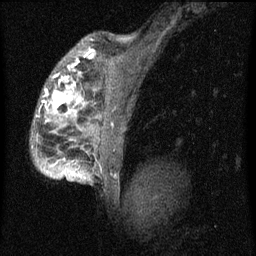
Breast MRI (dynamic contrast-enhanced), one sagittal slice; slice 48 of 60 in the series (ordered by position); dynamic contrast-enhanced series, image 2 of 4 at this slice position (ordered by acquisition); 1.5 T; TE 4.2 ms, TR 8 ms; 256 × 256 image matrix. Patient: female, 50 years.
Annotated regions visible in this slice (semi-automatically segmented with operator editing):
- analysis volume of interest (the breast-tissue region the enhancement analysis was run in; not a lesion): box from (x=31, y=44) to (x=124, y=177) px
- tumour enhancement mask (voxels above the 70 % enhancement threshold inside the analysis volume of interest): (x=45, y=54)–(x=94, y=169)